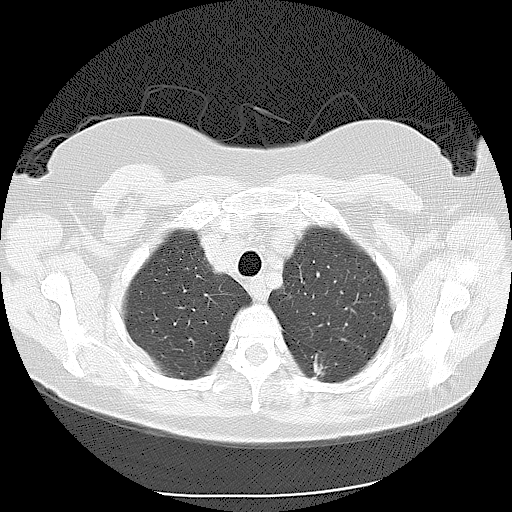
Axial slice from a low-dose chest CT screening exam. Second screening round (one year after baseline). Lung window (W 1500 / L -600 HU). 2.5 mm slice thickness. Female participant, aged 56 years at enrolment.
• Expert reader's lesion annotation, bounding box (x1, y1, x2, y2) in pixels: (290, 345, 342, 389).
• Reader record for this screening exam (exam-level; its link to the box is not recorded): non-calcified nodule or mass ≥4 mm, left lower lobe, 9 × 9 mm, spiculated (stellate) margins, soft tissue attenuation, pre-existing on the prior screen: yes; interval growth: yes.
• Official screen result: positive, other.
• Lung cancer was diagnosed 173 days after this screen: adenocarcinoma, NOS, left lower lobe, moderately differentiated (G2), stage IIA (AJCC 6th edition), 15 mm at pathology.